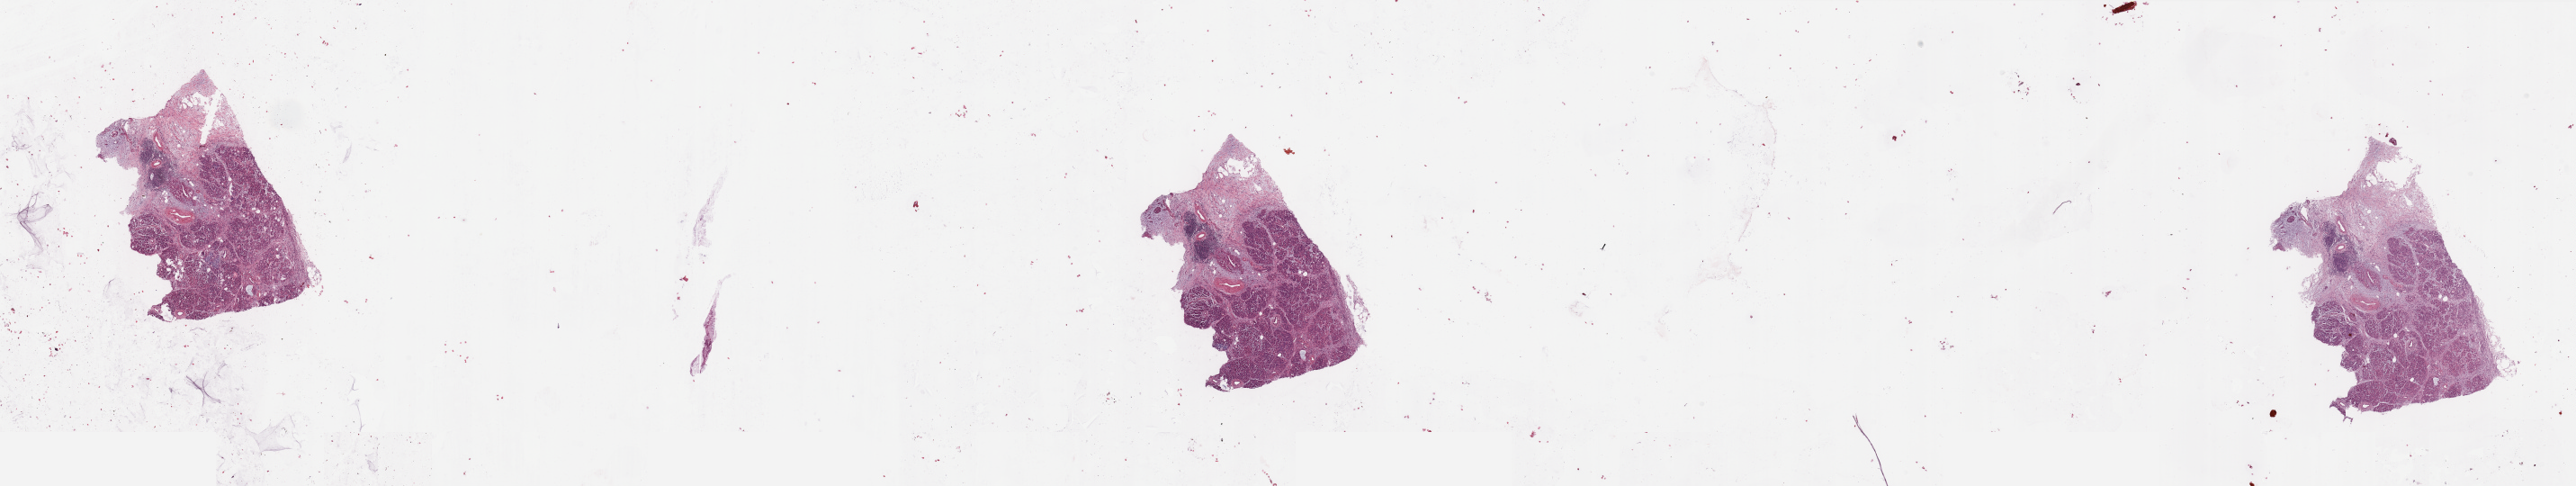
H&E-stained whole-slide image, whole scanned area (about 45.3 x 8.5 mm) shown as a low-resolution overview; pancreas, tumour tissue. Patient: female, age 74 years. Histologic grade: G3 (poorly differentiated).
Primary tumour site (as recorded): head. AJCC pathologic stage: III. Histologic diagnosis: Infiltrating duct carcinoma, NOS.